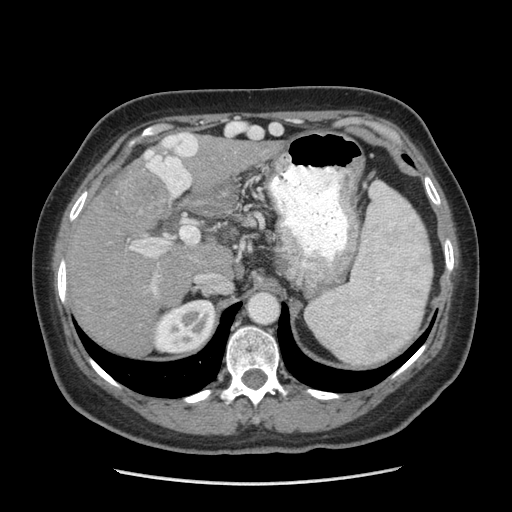
Contrast-enhanced abdominal CT (liver protocol), one axial slice. Slice 156 of 185 in the series (ordered by position). Reconstruction kernel STANDARD. Soft-tissue window (W 400 / L 40 HU). 512 × 512 image matrix, field of view 360 × 360 mm. From the clinical record (not read from this slice): diagnosis: hepatocellular carcinoma (patient treated with transarterial chemoembolisation; whether this scan precedes or follows treatment is not stated here); TNM stage (as recorded): Stage-I; Child-Pugh class: A; tumour nodularity: uninodular.
Structures marked on this image (semi-automatic segmentation, software-assisted and operator-edited):
- liver parenchyma outside the tumour (the mass and vessels are separate outlines, so this box may not span the whole liver): bounding box <66,139,270,354> (left, top, right, bottom; pixels)
- mass: <111,164,170,223>
- liver vessels: <130,162,192,292>